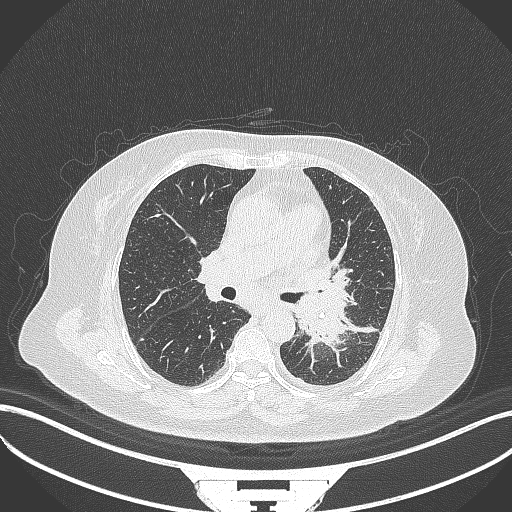
Chest CT, one axial slice. Position 198 of 322 along the scan axis. Reconstruction kernel B70f. 120 kVp. Lung window (W 1500 / L -600 HU). 1 mm slice thickness. 512 × 512 image matrix, field of view 400 × 400 mm. Patient: female, 69 years. From the clinical record (not read from this slice): clinical TNM (as recorded): T2b N3 M1.
Annotated regions visible in this slice (rectangle marked by the reading radiologist):
- lung tumour (recorded histology: adenocarcinoma): bounding box [x1, y1, x2, y2] px = [290, 286, 352, 352]